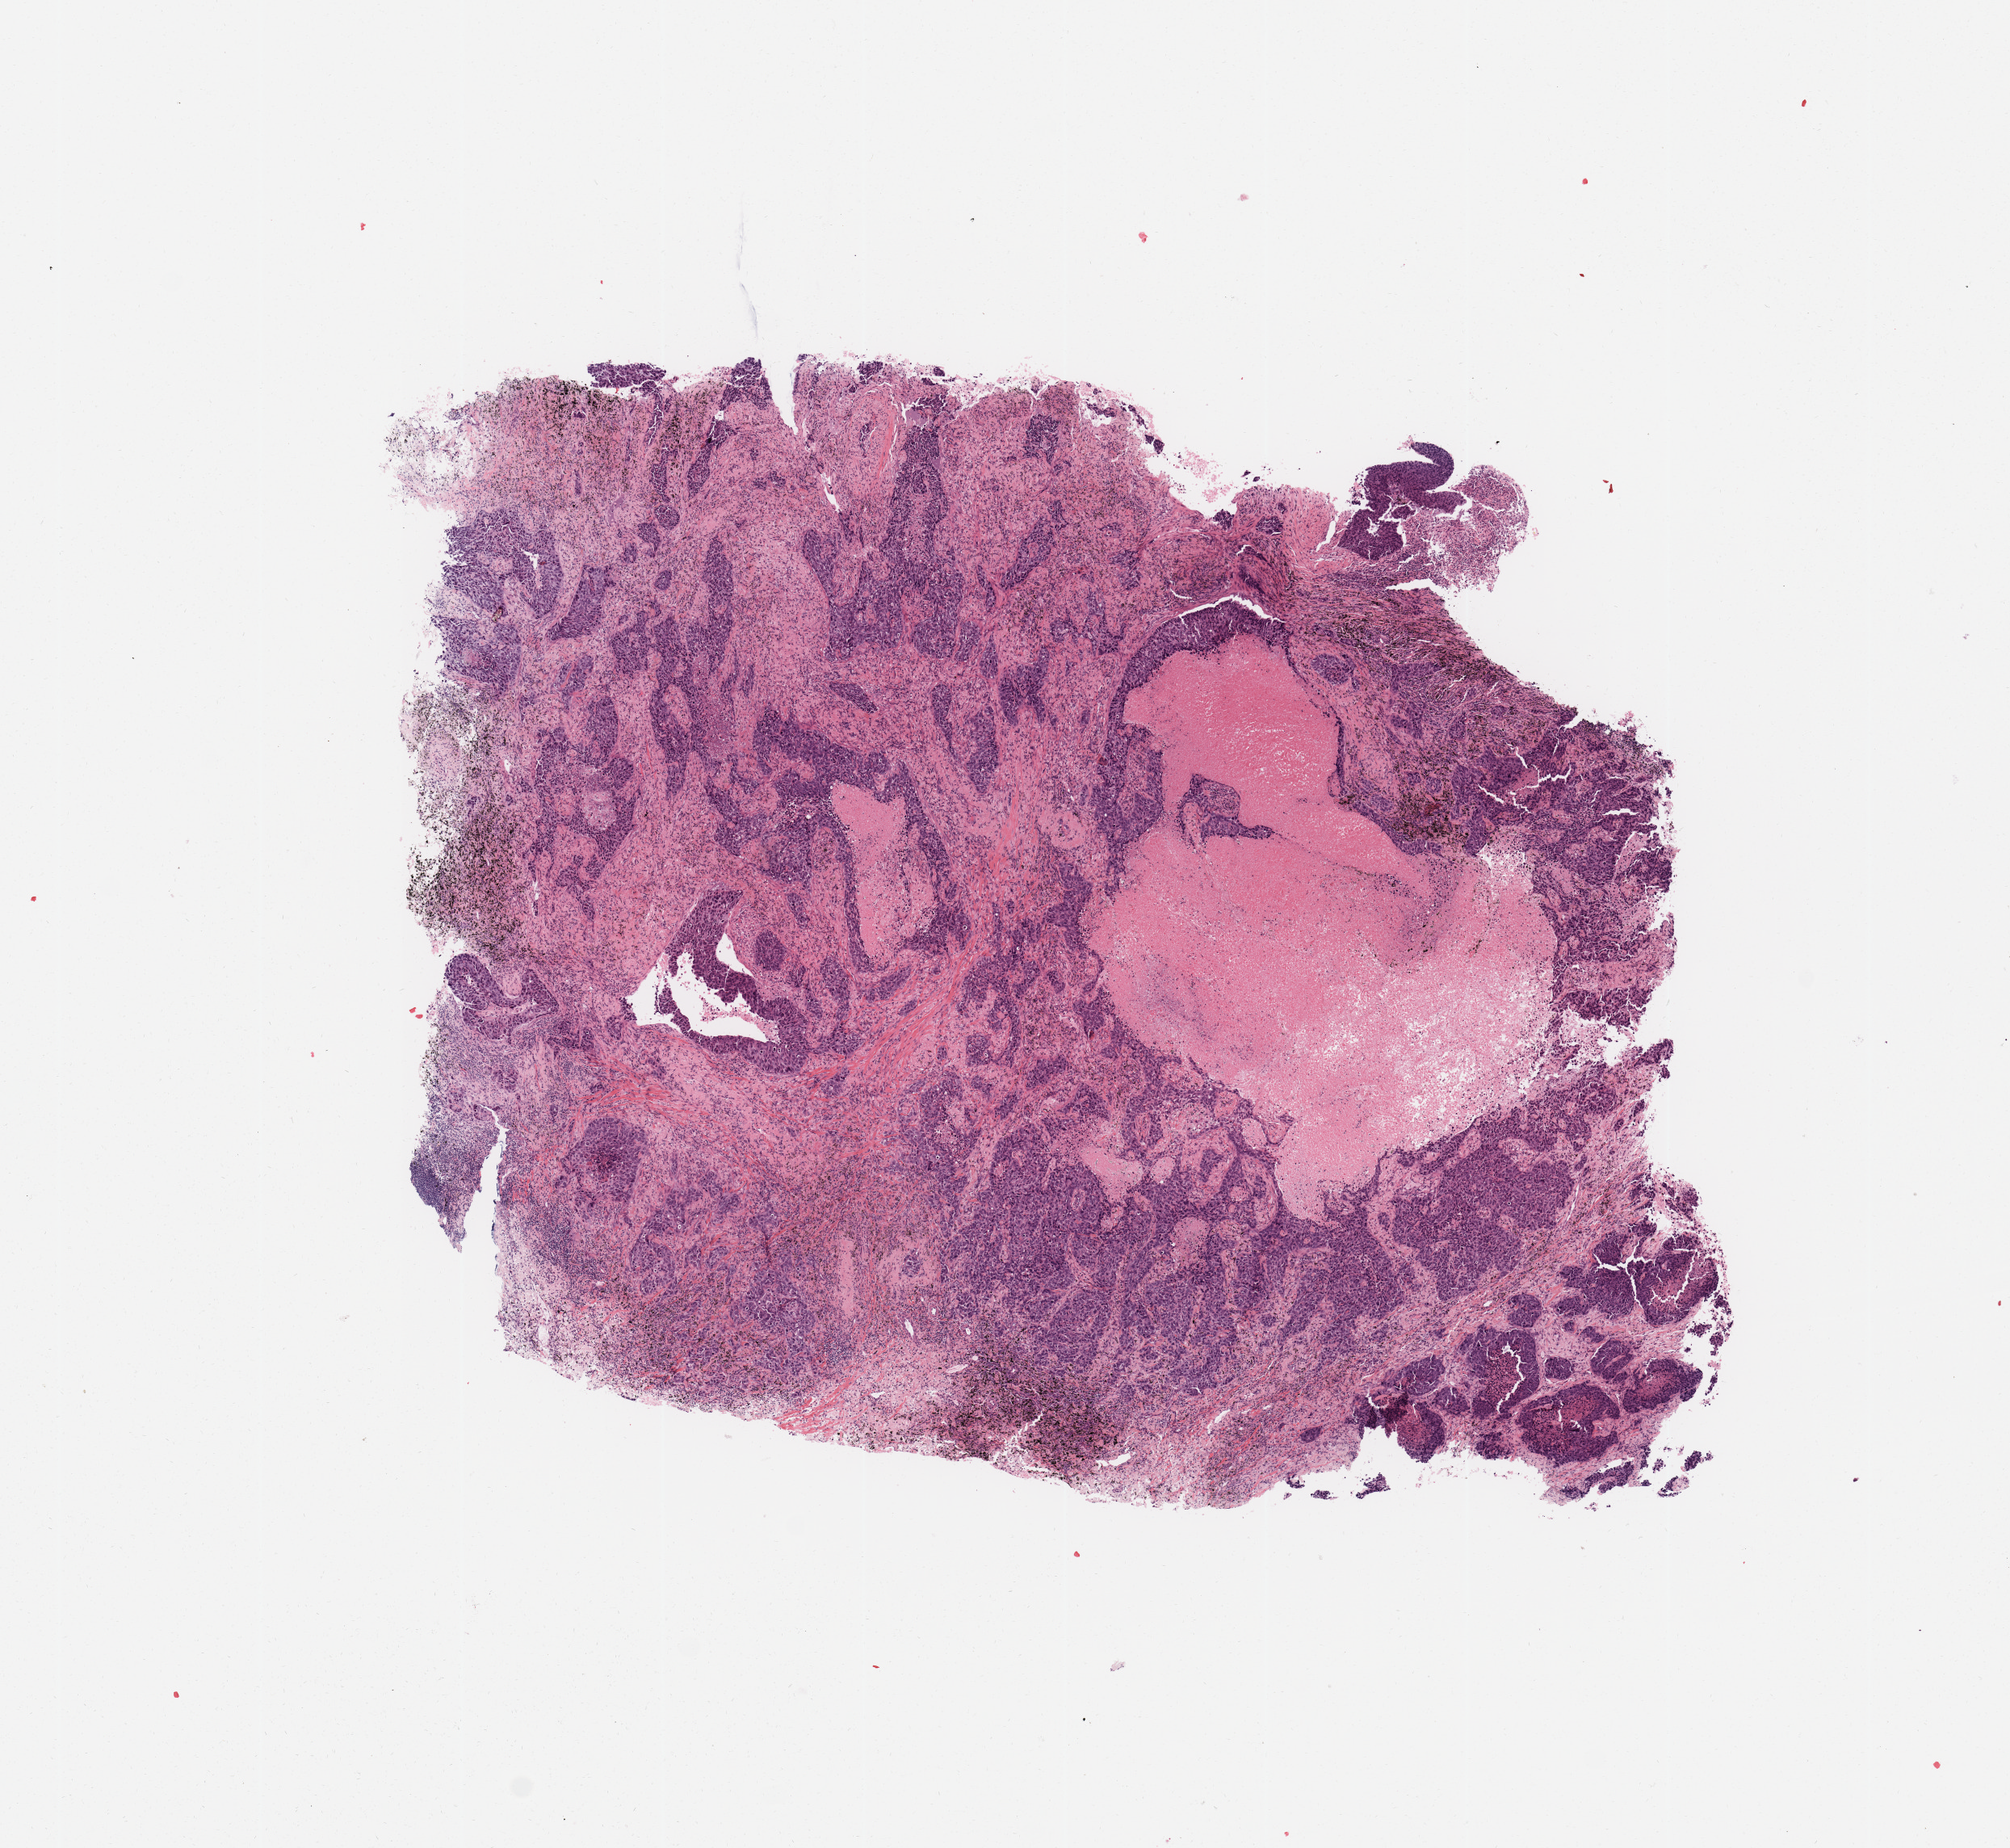
Digitized H&E-stained tissue section (whole slide), a low-resolution overview of the entire scanned area, about 9.8 x 9.0 mm. Tumour tissue sample, lung. Patient: male, age 68 years. Histologic grade: G3 (poorly differentiated).
• diagnosis: Squamous cell carcinoma, NOS
• AJCC pathologic stage: IIA
• primary tumour site (as recorded): left upper lobe